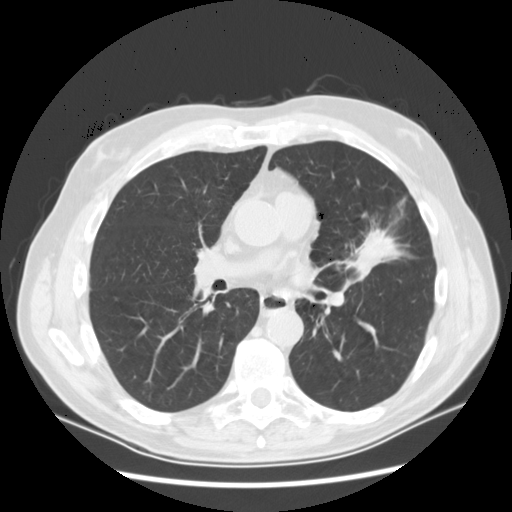
Axial slice from a low-dose chest CT screening exam; baseline annual screen; lung window (W 1500 / L -600 HU); 2.5 mm slice thickness; standard (soft-tissue) reconstruction kernel (STANDARD); slice 62 of 132 in the series. Male participant, aged 65 years at enrolment.
• Expert-annotated lung lesion, bounding box (x1, y1, x2, y2) in pixels: (348, 206, 415, 276).
• Screening reader's record for this exam (one nodule recorded; not confirmed to be the boxed lesion): non-calcified nodule or mass ≥4 mm, left upper lobe, 37 × 27 mm, spiculated (stellate) margins, soft tissue attenuation.
• Participant outcome: lung cancer diagnosed 56 days after this screen — non-small cell carcinoma, poorly differentiated (G3), stage IA (AJCC 6th edition).